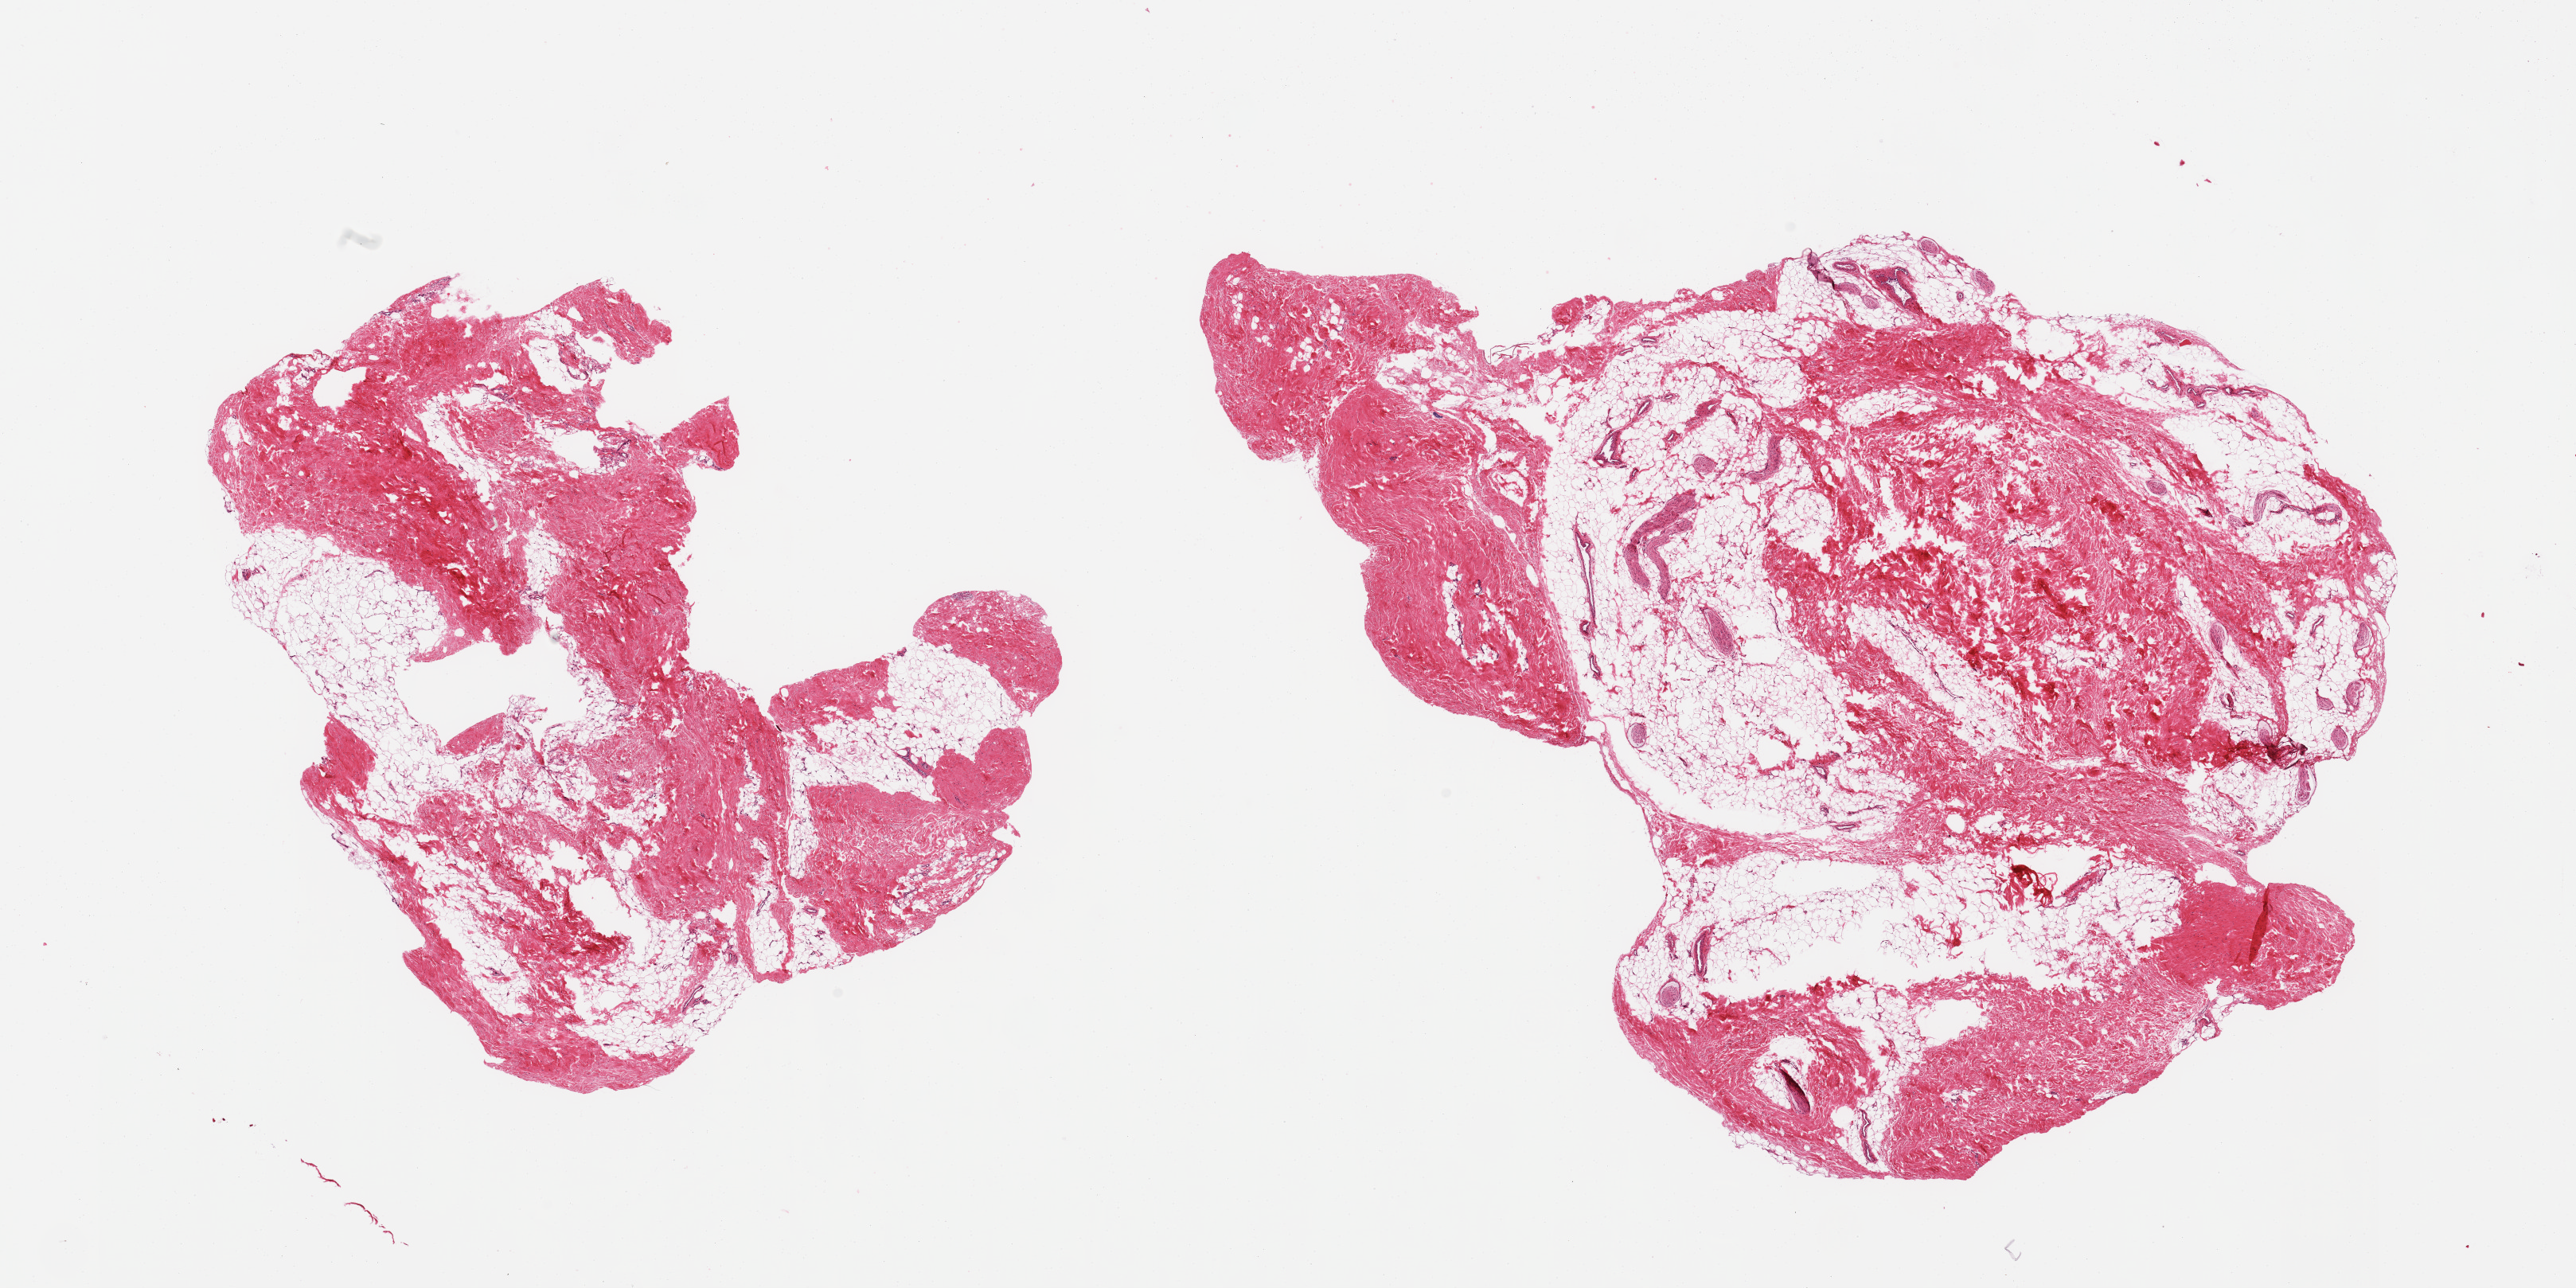
Digitized H&E-stained section, brightfield — shown as a low-resolution overview of the whole scanned area (about 25.6 x 12.8 mm); PAXgene-fixed, paraffin-embedded tissue; sampled site (target tissue): breast; tissue donor sample.
Review note (as recorded): 2 pieces; ~60% fibrovascular and neural tissue and ~40% adipose tissues; no ductal structures seen.